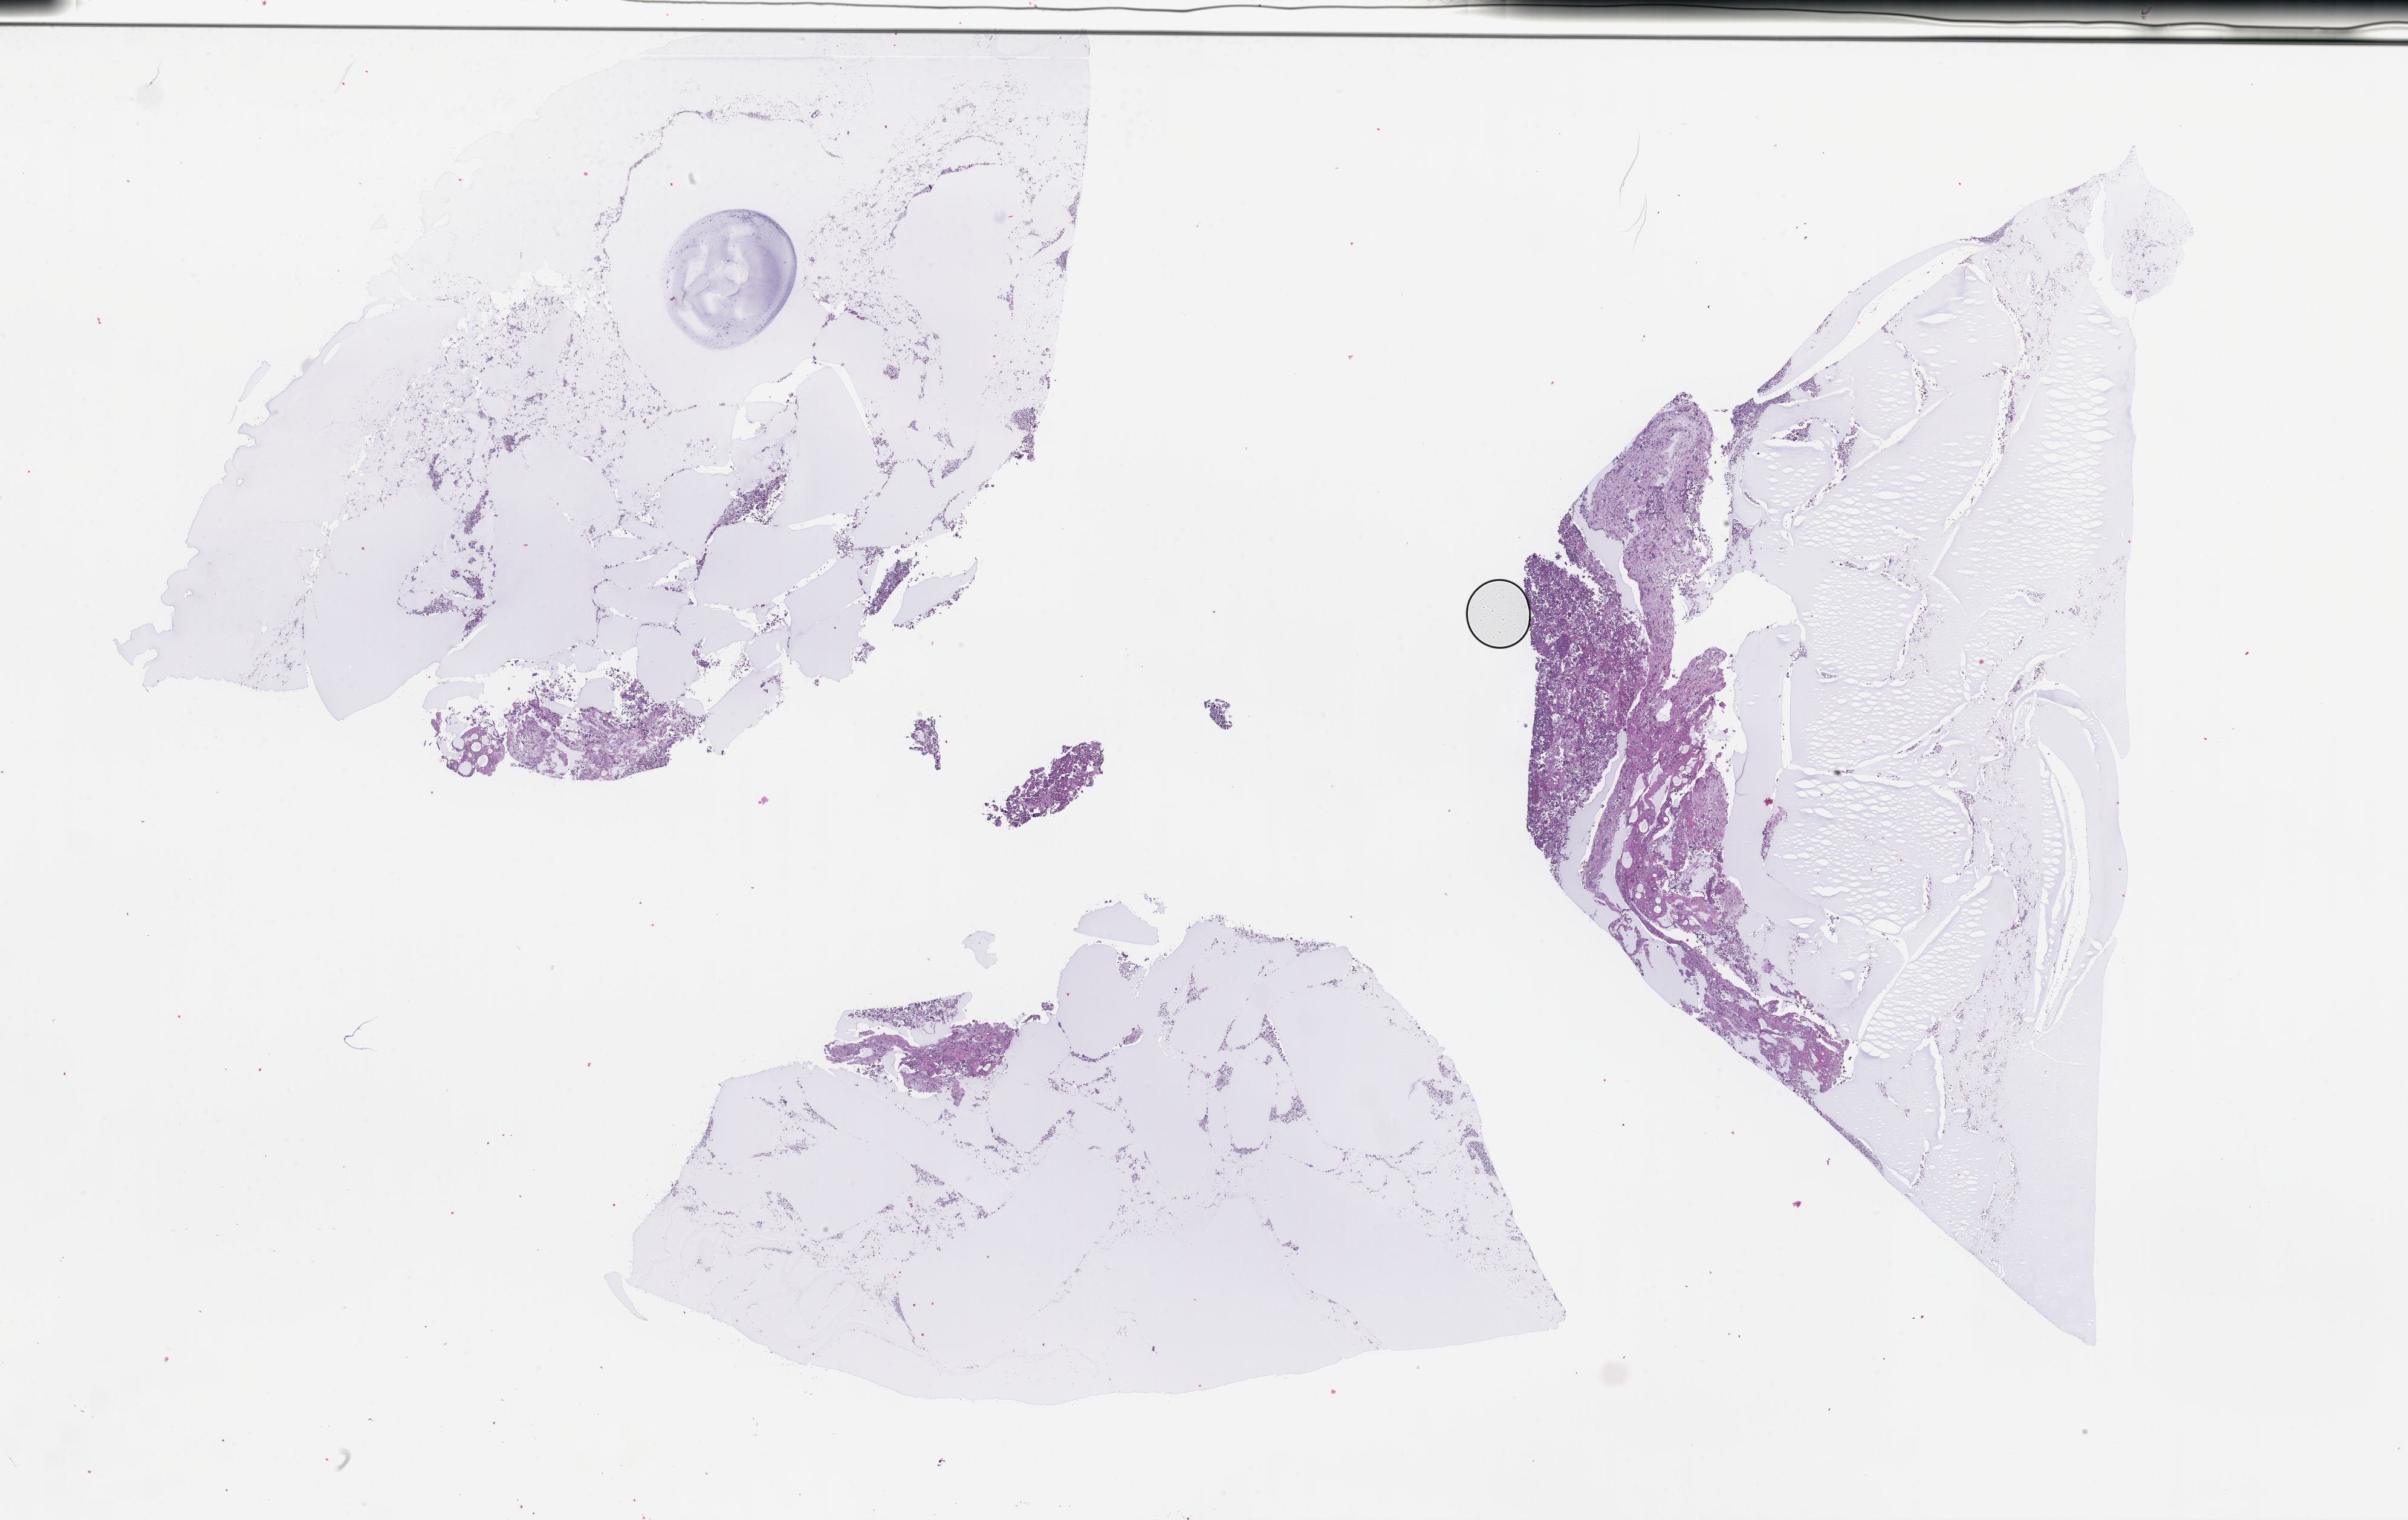
Haematoxylin and eosin whole-slide image, low-resolution overview of the scanned area, about 32.2 x 20.3 mm, formalin-fixed, paraffin-embedded (FFPE) tissue, specimen time point: archival tissue. Patient sex: male.
This section: metastasis (sampled organ not recorded). Primary diagnosis of the patient: Non-Small Cell Lung Carcinoma.